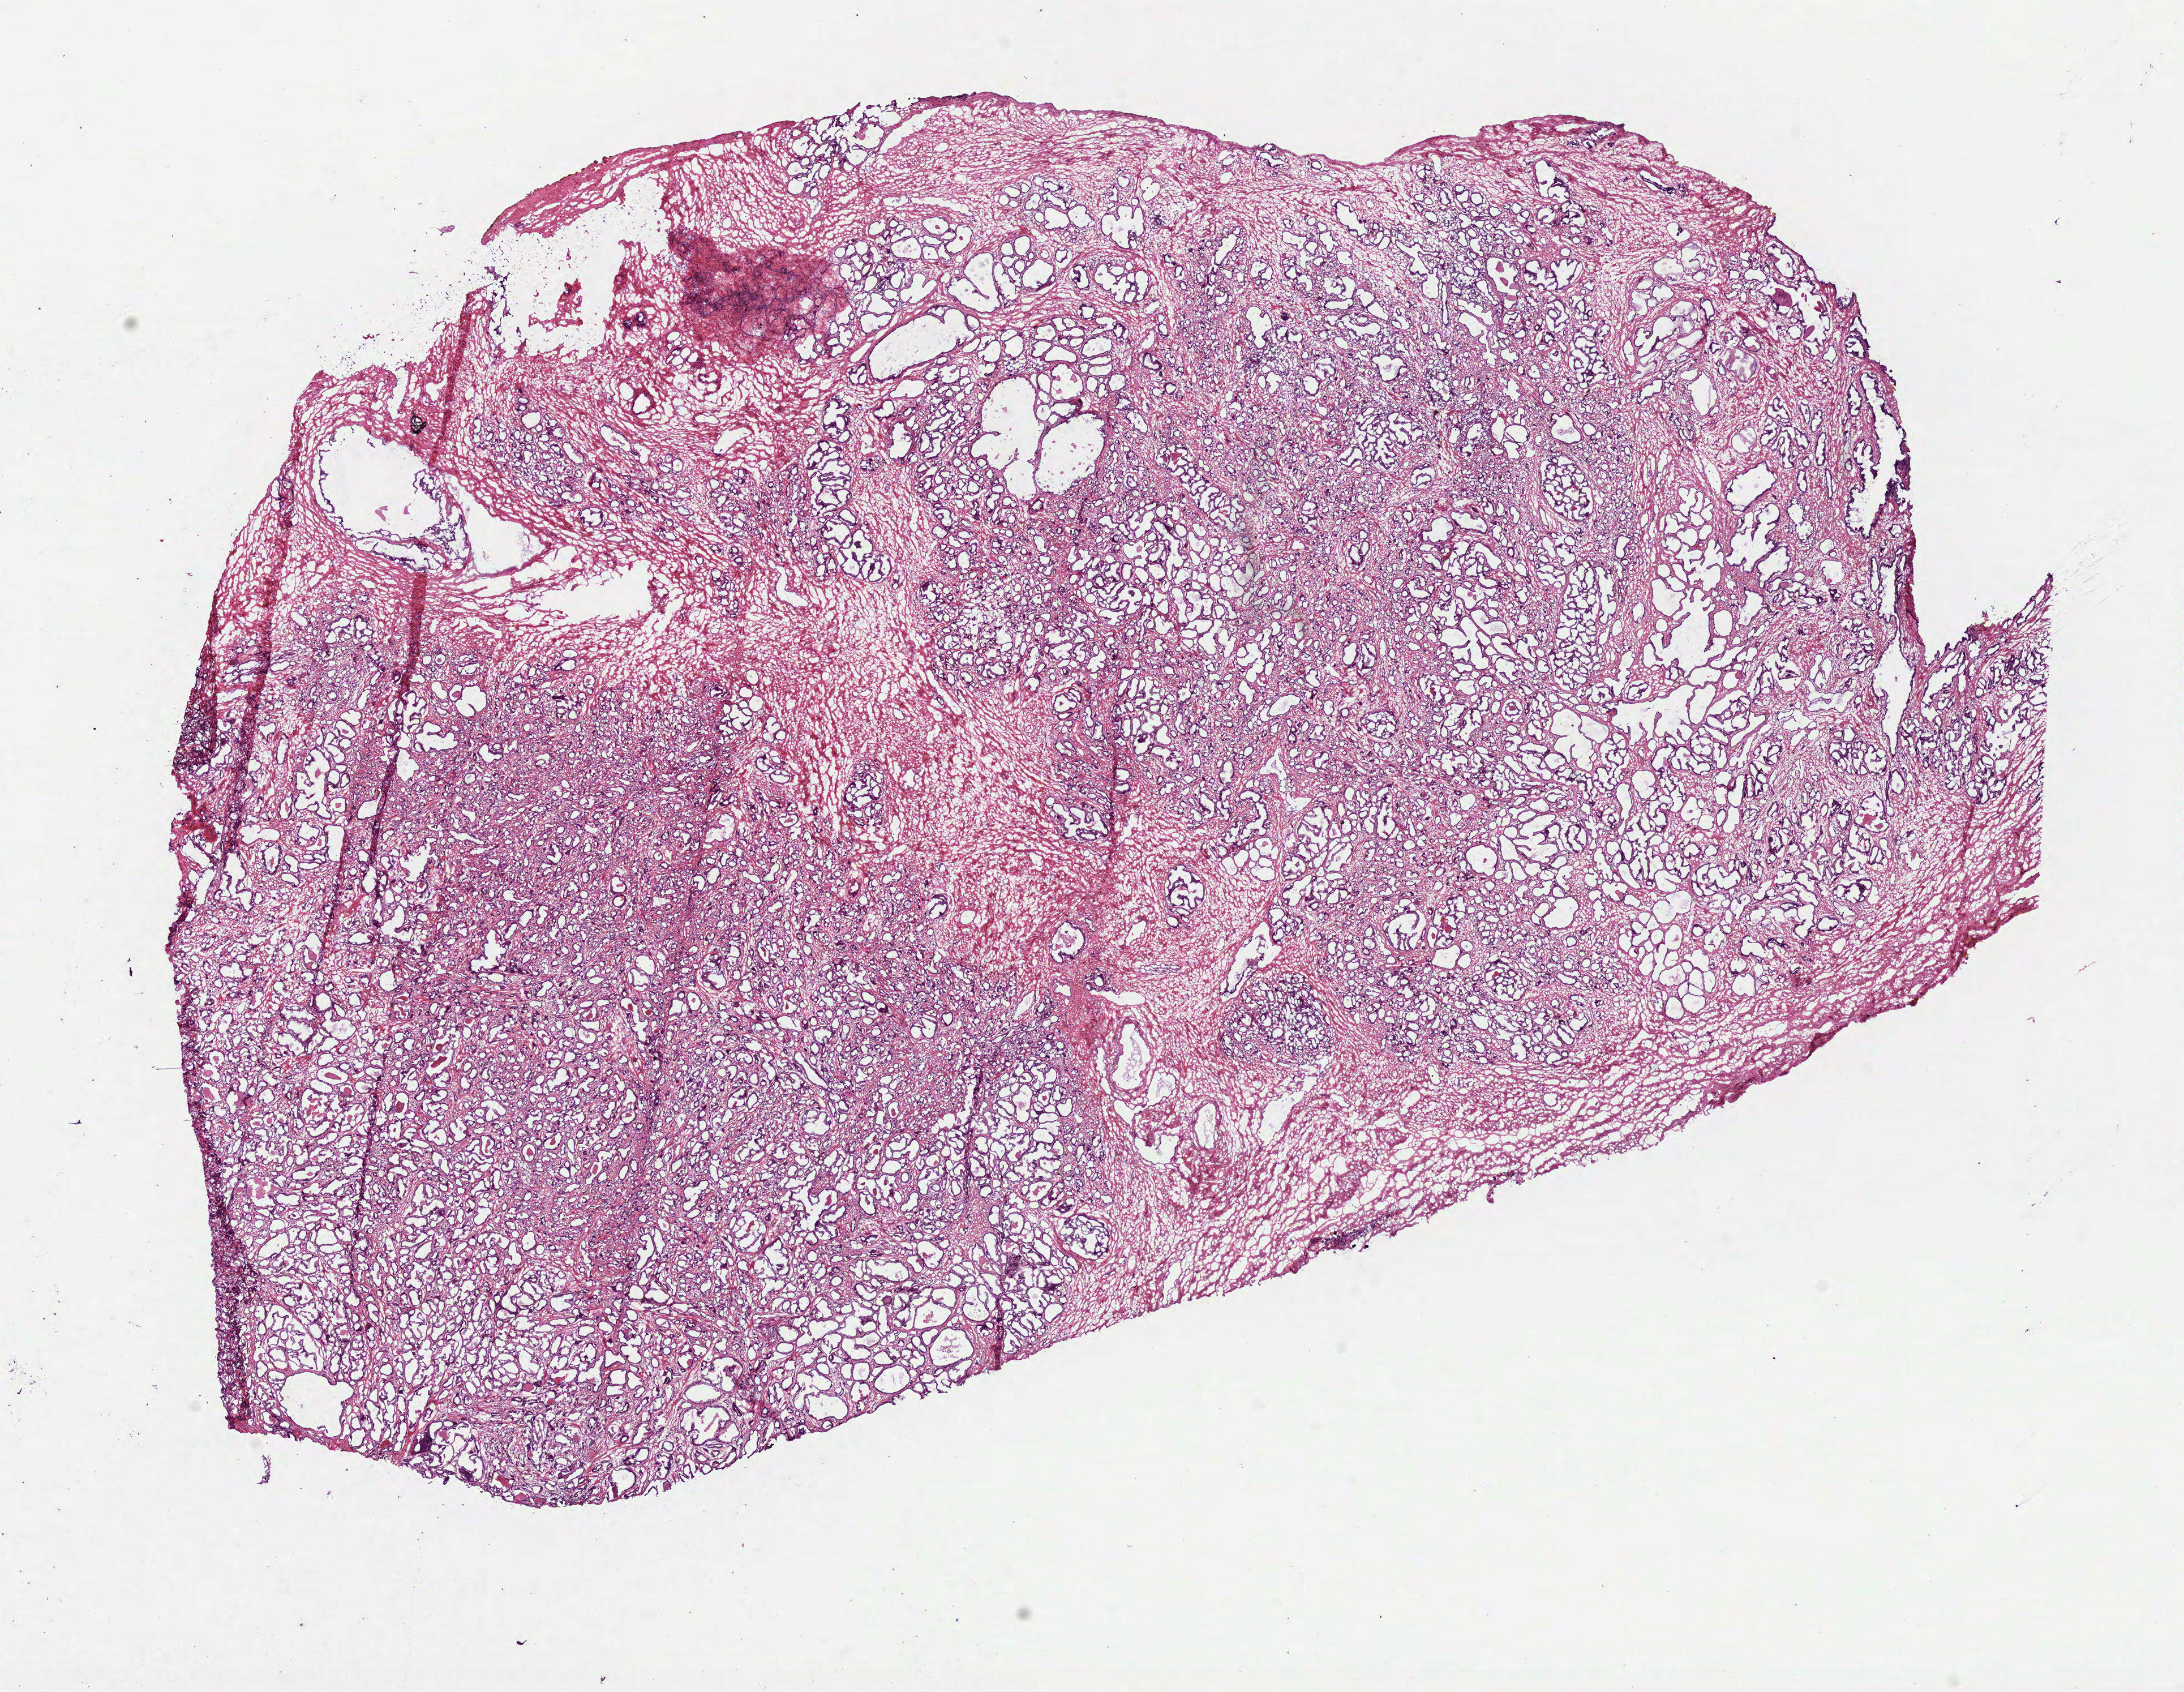
Whole-slide histology image, H&E-stained — shown as a low-resolution overview of the whole scanned area (about 15.6 x 12.1 mm, slide scanned at 40x); frozen section; primary tumour sample from the prostate. Patient: male, age at initial diagnosis 72 years. Gleason score: 7 (3+4). Pathologist review of this section (percent, as recorded): tumour cells 75%, tumour nuclei 75%, normal cells 15%, stromal cells 10%, necrosis 0%. Inflammatory infiltration, as recorded: lymphocyte infiltration 2%, monocyte infiltration 0%, neutrophil infiltration 0%.
Laterality: bilateral. Histologic diagnosis: Acinar cell carcinoma. Lymph nodes positive (case pathology): 0 of 25 examined.